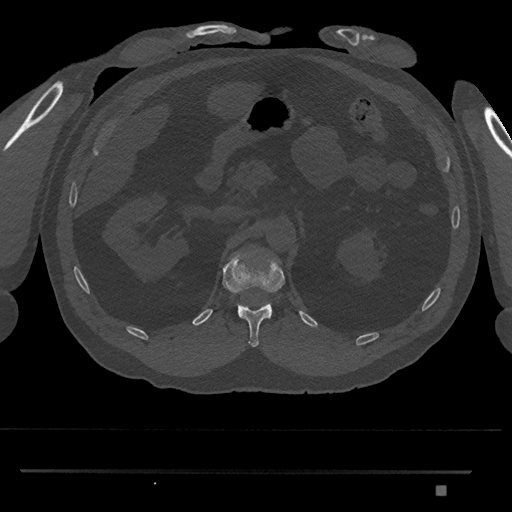
CT including the spine, one axial slice; position 871 of 1134 along the scan axis; bone window (W 1800 / L 400 HU); 0.5 mm slice thickness; 512 × 512 image matrix, field of view 429 × 429 mm. Male patient, age 65 years. From the clinical record (not read from this slice): primary cancer: prostate.
Outlined on this slice (semi-automatically segmented with operator editing):
- L1 vertebra: bounding box [x1, y1, x2, y2] px = [270, 306, 272, 317]
- T12 vertebra: [222, 256, 285, 347]